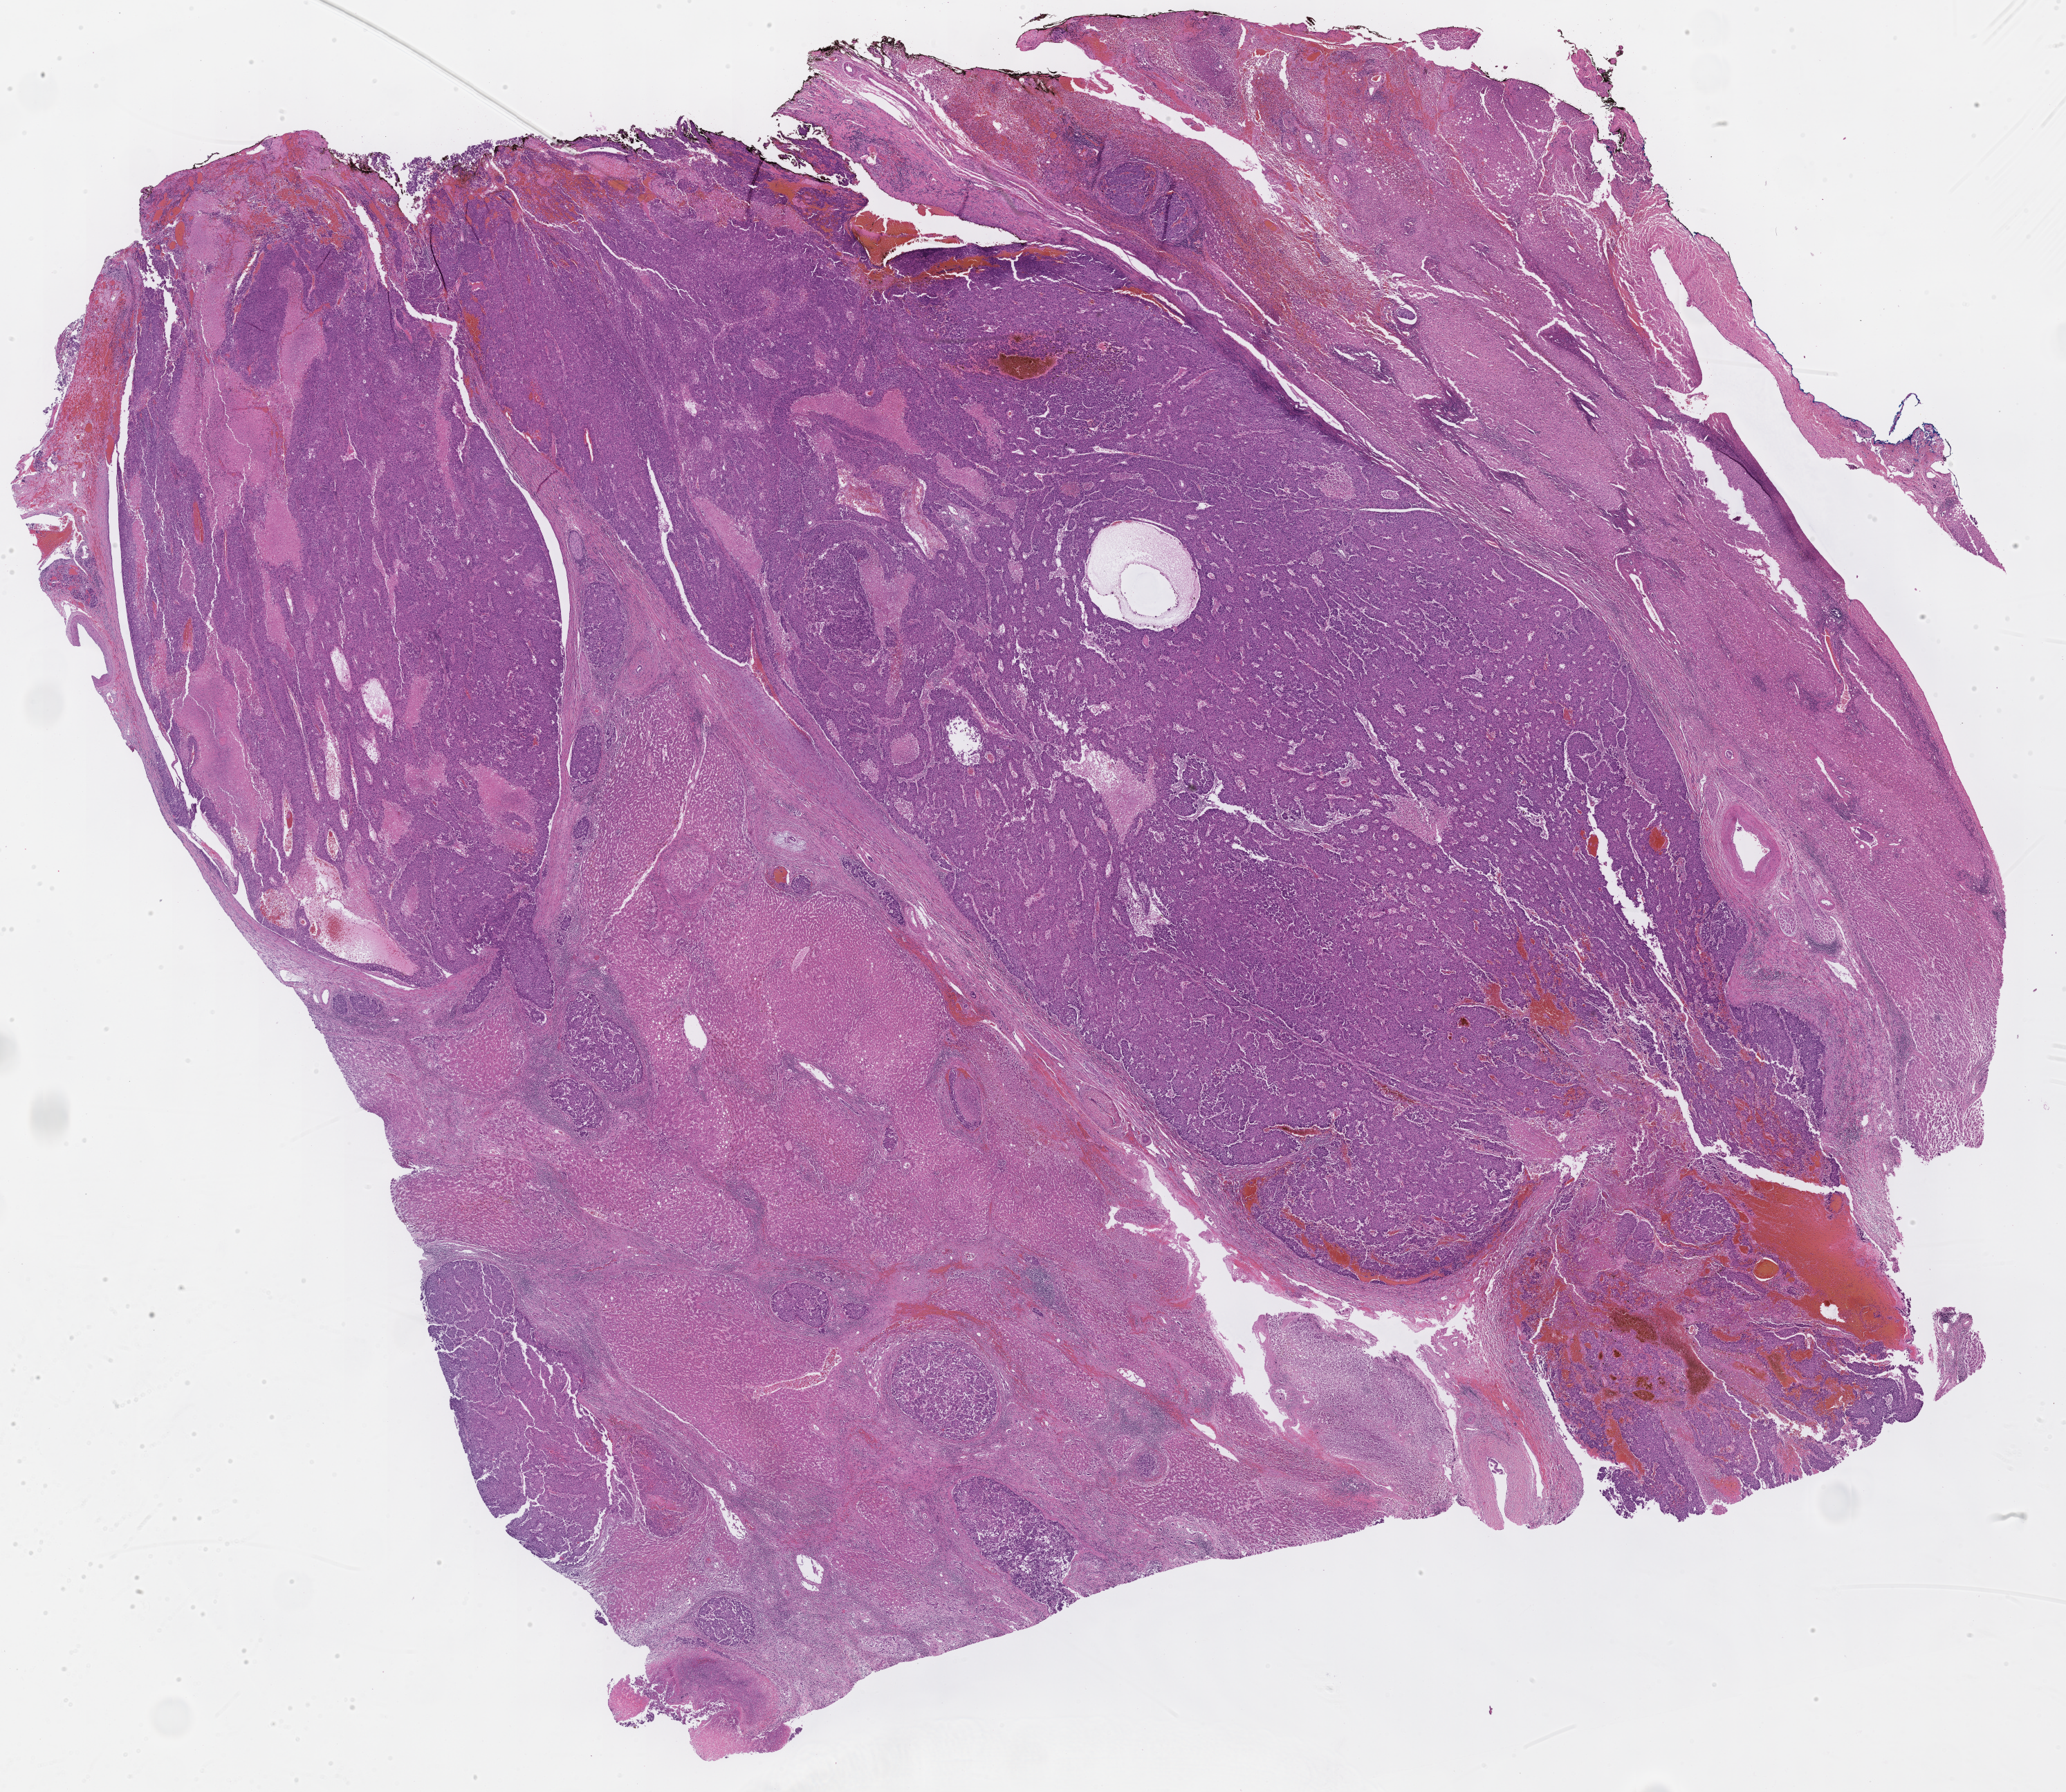
Hematoxylin and eosin (H&E) stained whole-slide image, a low-resolution overview of the entire scanned area, about 24.2 x 21.0 mm (slide scanned at 40x), formalin-fixed paraffin-embedded (FFPE) diagnostic section, sample: primary tumour, liver. Patient: male, age at initial diagnosis 75 years.
Pathologic diagnosis: Hepatocellular carcinoma, NOS.